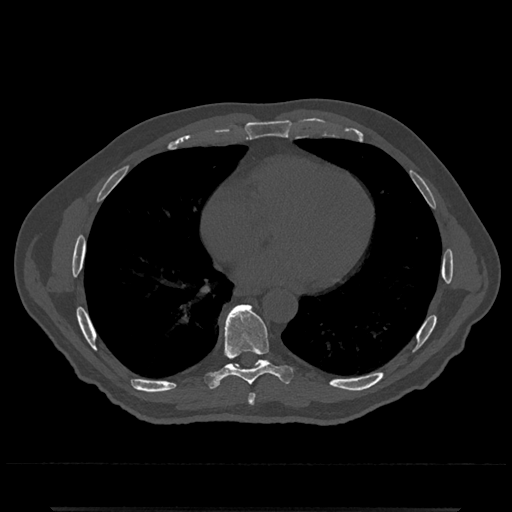
CT including the spine, one axial slice; position 666 of 797 along the scan axis; bone window (W 1800 / L 400 HU); 0.5 mm slice thickness; 512 × 512 image matrix, field of view 393 × 393 mm. Patient: male, 67 years. Case-level facts recorded for this patient, not image findings: primary cancer: prostate.
Structures marked on this image (semi-automatic segmentation, software-assisted and operator-edited):
- T7 vertebra: bounding box <248,393,255,405> (left, top, right, bottom; pixels)
- T8 vertebra: <205,304,293,388>